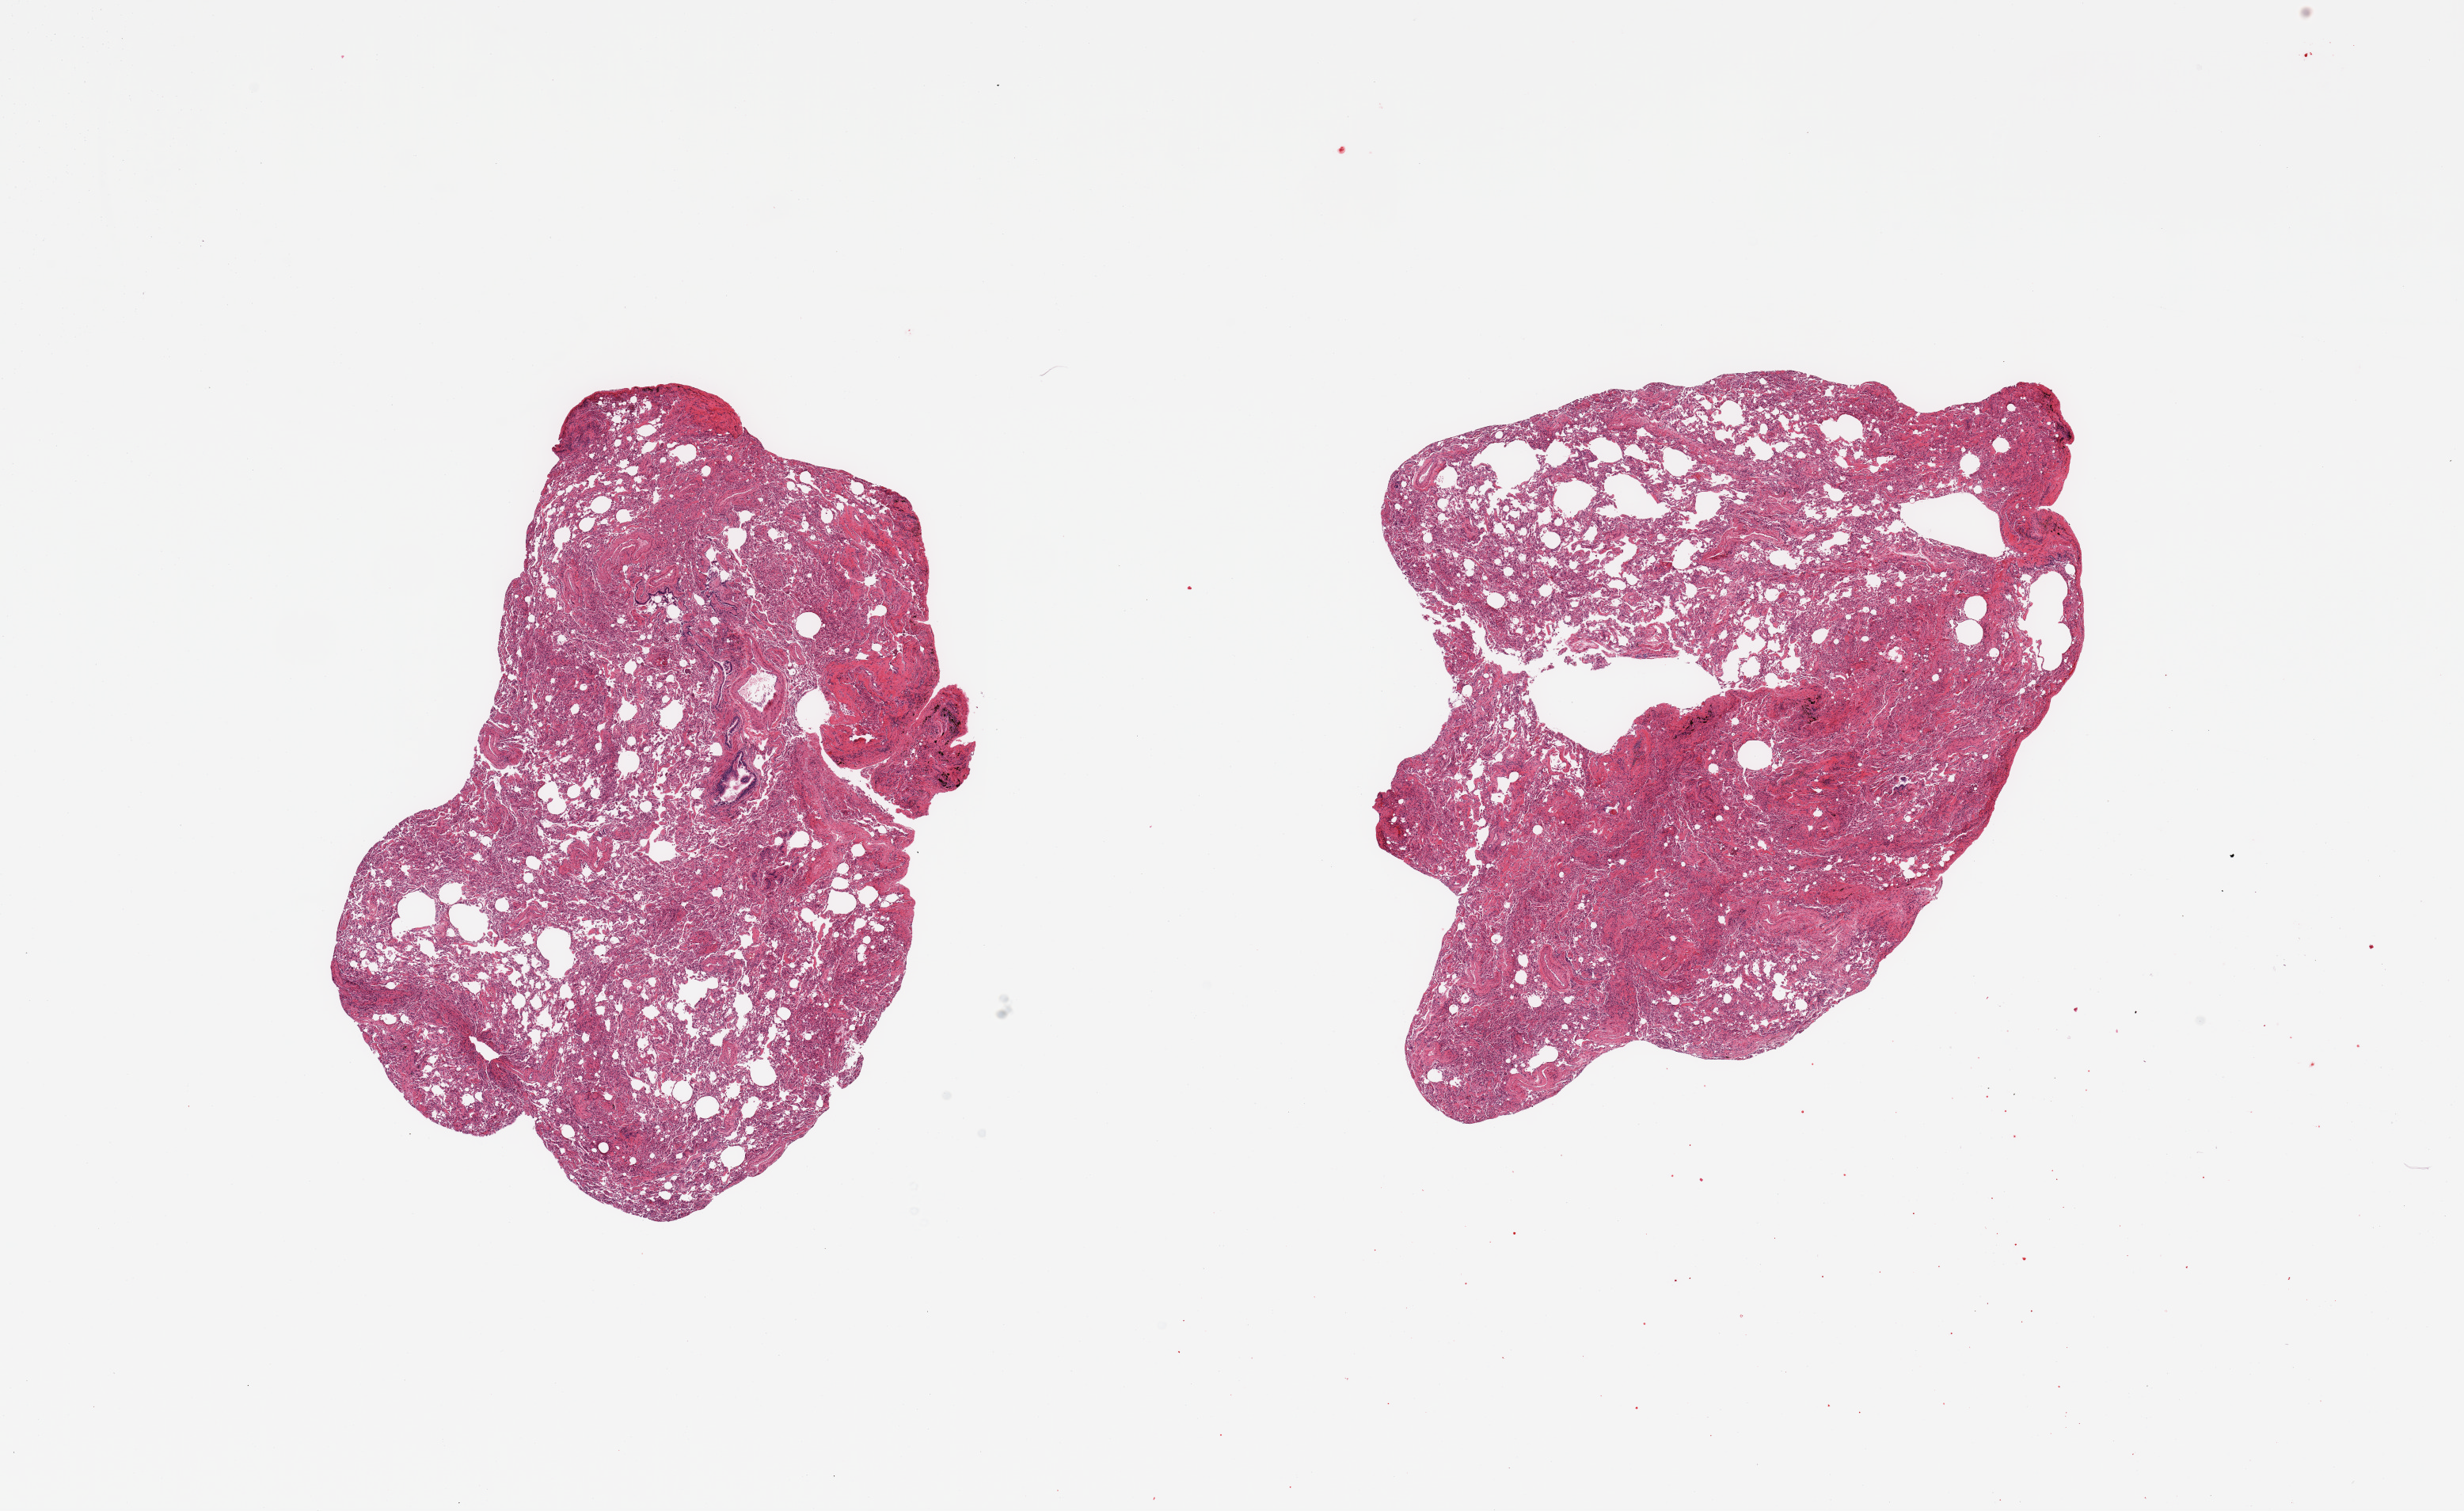
Whole-slide image, H&E stain, brightfield — shown as a low-resolution overview of the whole scanned area (about 24.6 x 15.1 mm), PAXgene-fixed paraffin-embedded (PFPE) section, section of lung (target tissue), donor tissue sample. Donor sex: male.
* pathologist's review note for this sample: 2 pieces; patchy areas of interstitial fibrosis